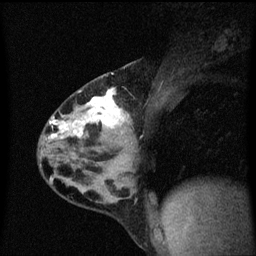
Breast MRI (dynamic contrast-enhanced), one sagittal slice. Position 35 of 60 along the scan axis. Dynamic contrast-enhanced series, image 2 of 3 at this slice position (ordered by acquisition). 1.5 T. TE 4.2 ms, TR 8.4 ms. 256 × 256 image matrix, field of view 200 × 200 mm. Female patient, age 32 years.
Annotated regions visible in this slice (semi-automatic segmentation, software-assisted and operator-edited):
- analysis volume of interest (the breast-tissue region the enhancement analysis was run in; not a lesion): bounding box <38,74,149,169> (left, top, right, bottom; pixels)
- tumour enhancement mask (voxels above the 70 % enhancement threshold inside the analysis volume of interest): <49,88,130,155>